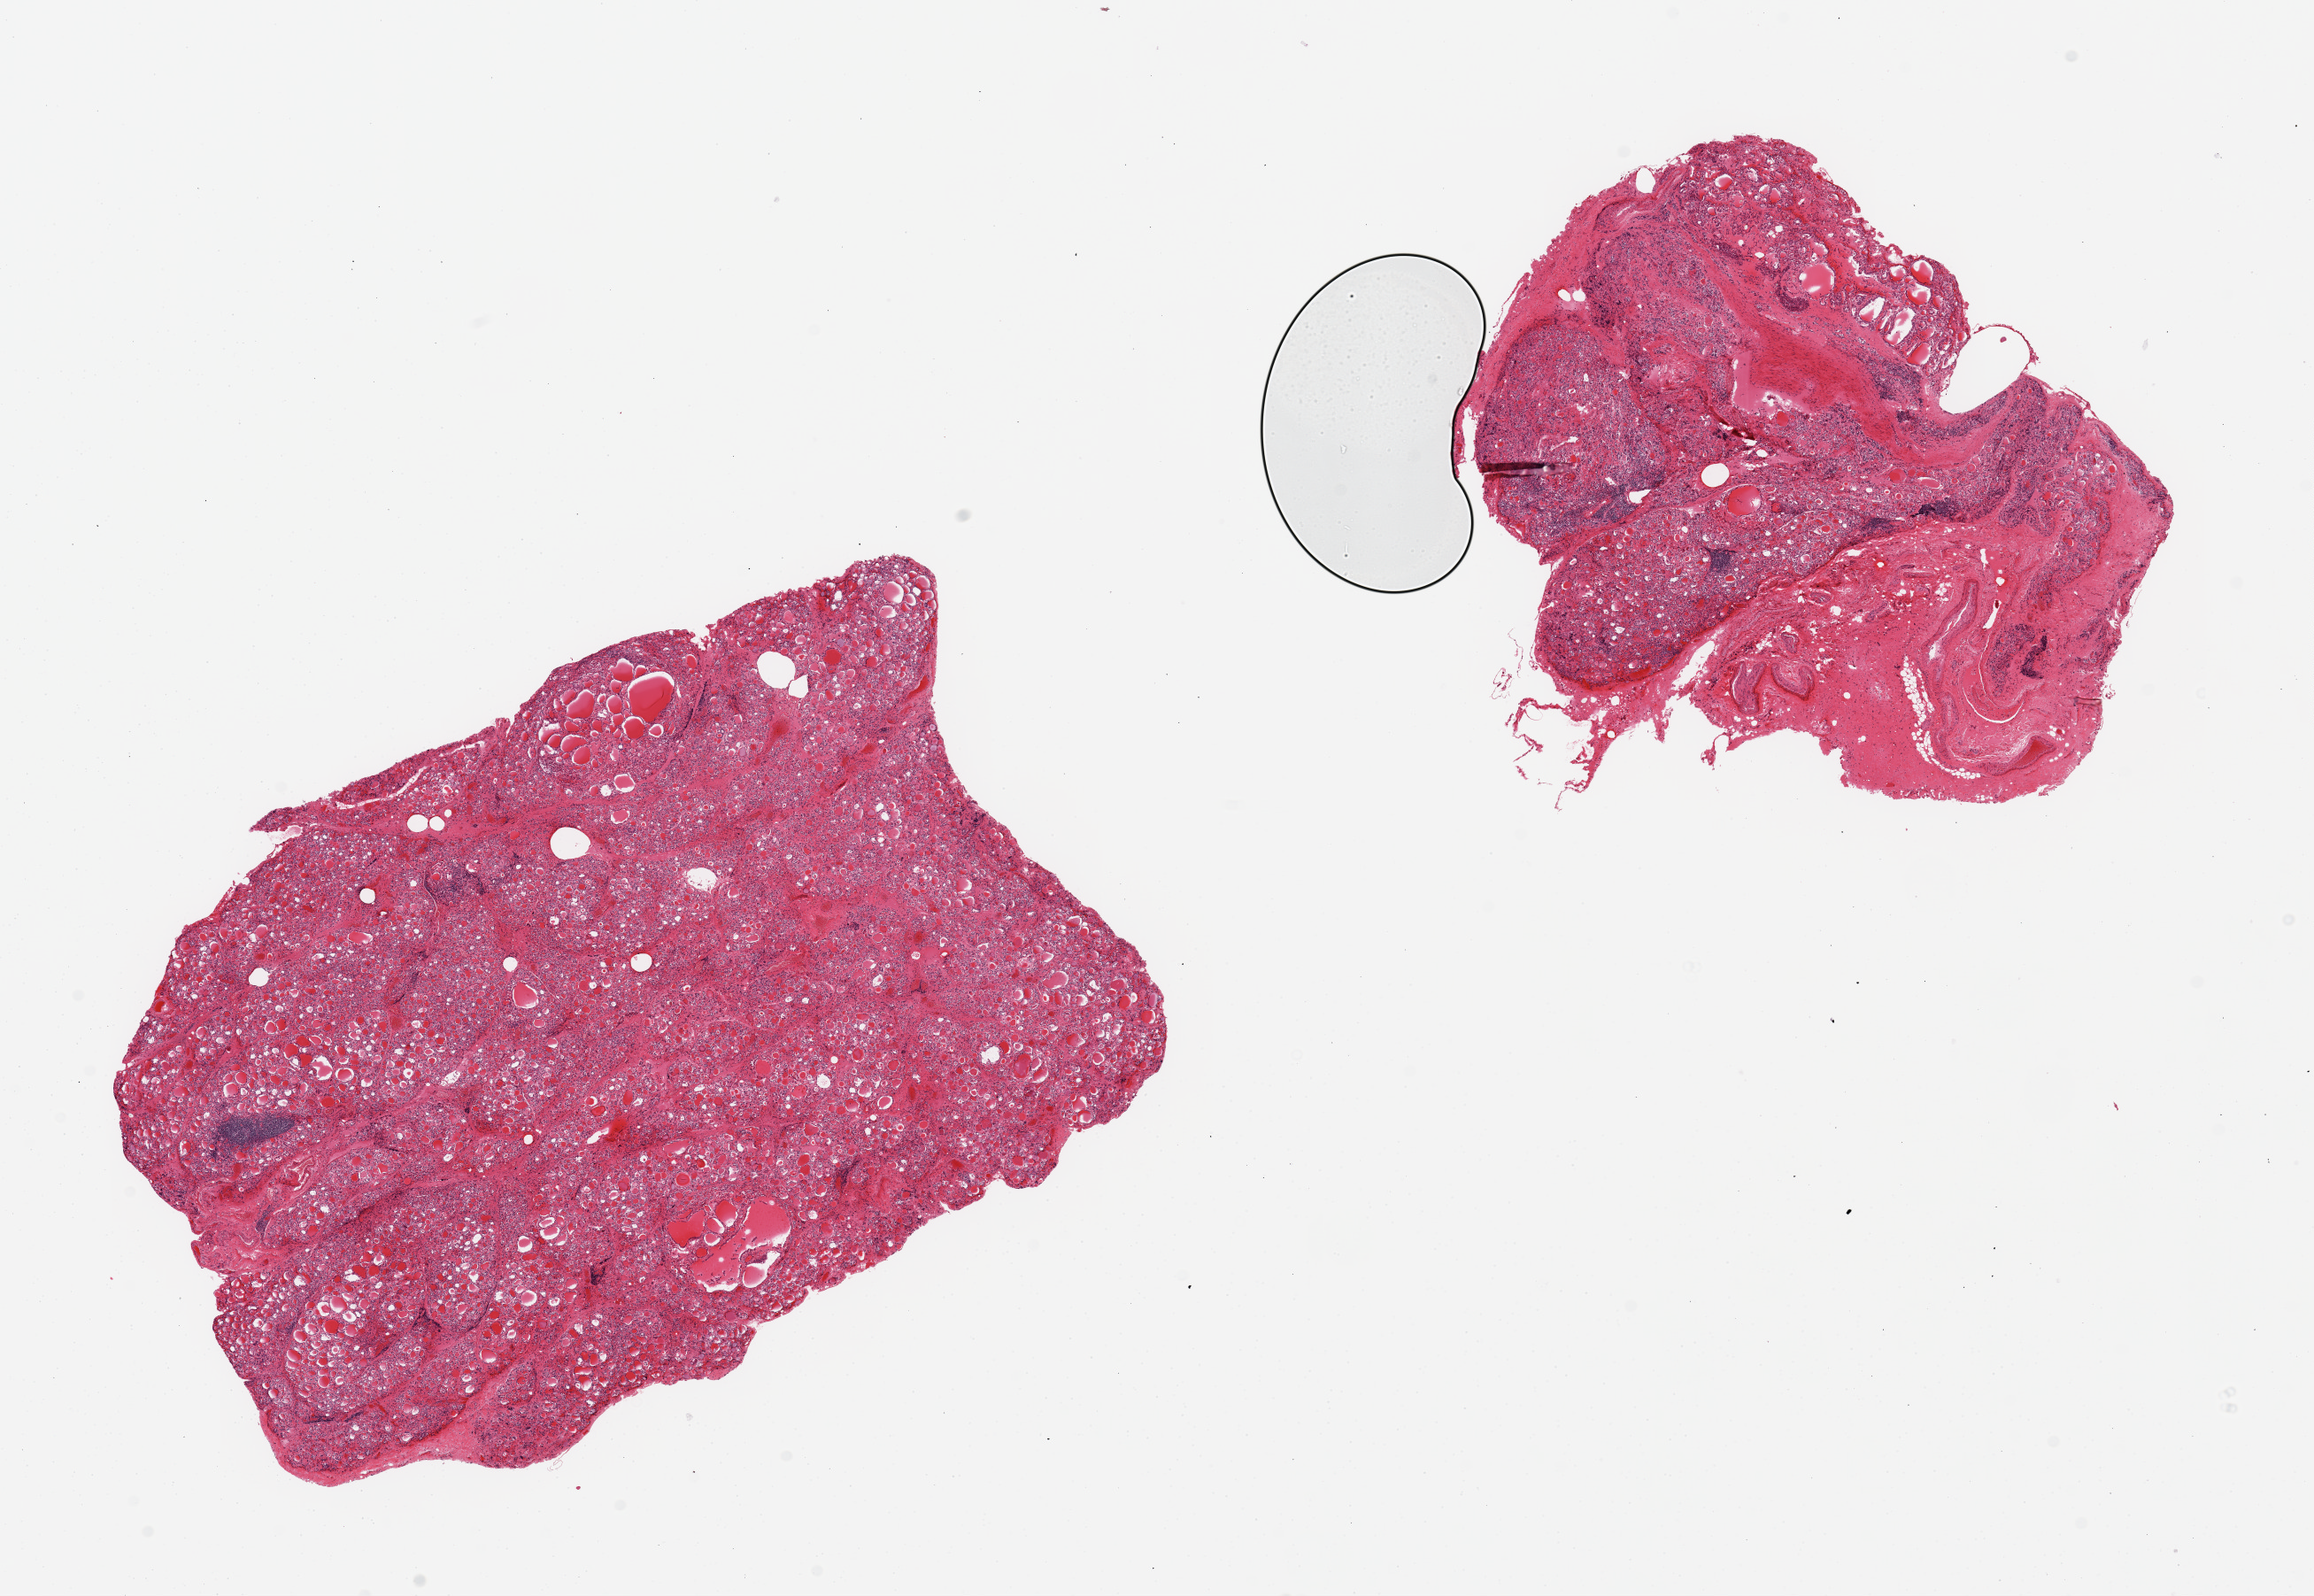
Whole-slide image, hematoxylin and eosin (H&E) stain, brightfield — shown as a low-resolution overview of the whole scanned area (about 20.7 x 14.3 mm); PAXgene-fixed paraffin-embedded (PFPE) section; target tissue: thyroid; tissue donor sample. Female donor.
• reviewer comment on this tissue sample: 2 pieces; fibrosis with nodularity, thyroid follicles and scattered aggregates of lymphocytes (likely Hashimoto's thyroiditis); one piece includes ~30% of fibrous tissue and large vessels